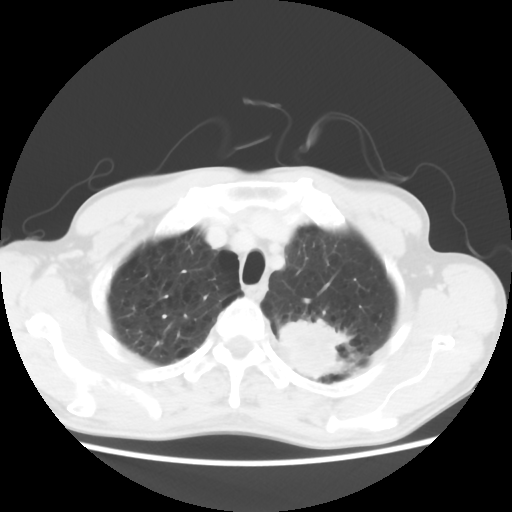
Chest CT, one axial slice; position 54 of 64 along the scan axis; reconstruction kernel STANDARD; 120 kVp; lung window (W 1500 / L -600 HU); 512 × 512 image matrix. Patient: male, 63 years. Case-level facts recorded for this patient, not image findings: clinical TNM (as recorded): T2 N0 M0.
Outlined on this slice (bounding box drawn by a radiologist):
- lung tumour (recorded histology: adenocarcinoma): bounding box (x1, y1, x2, y2) in pixels: (274, 314, 353, 383)